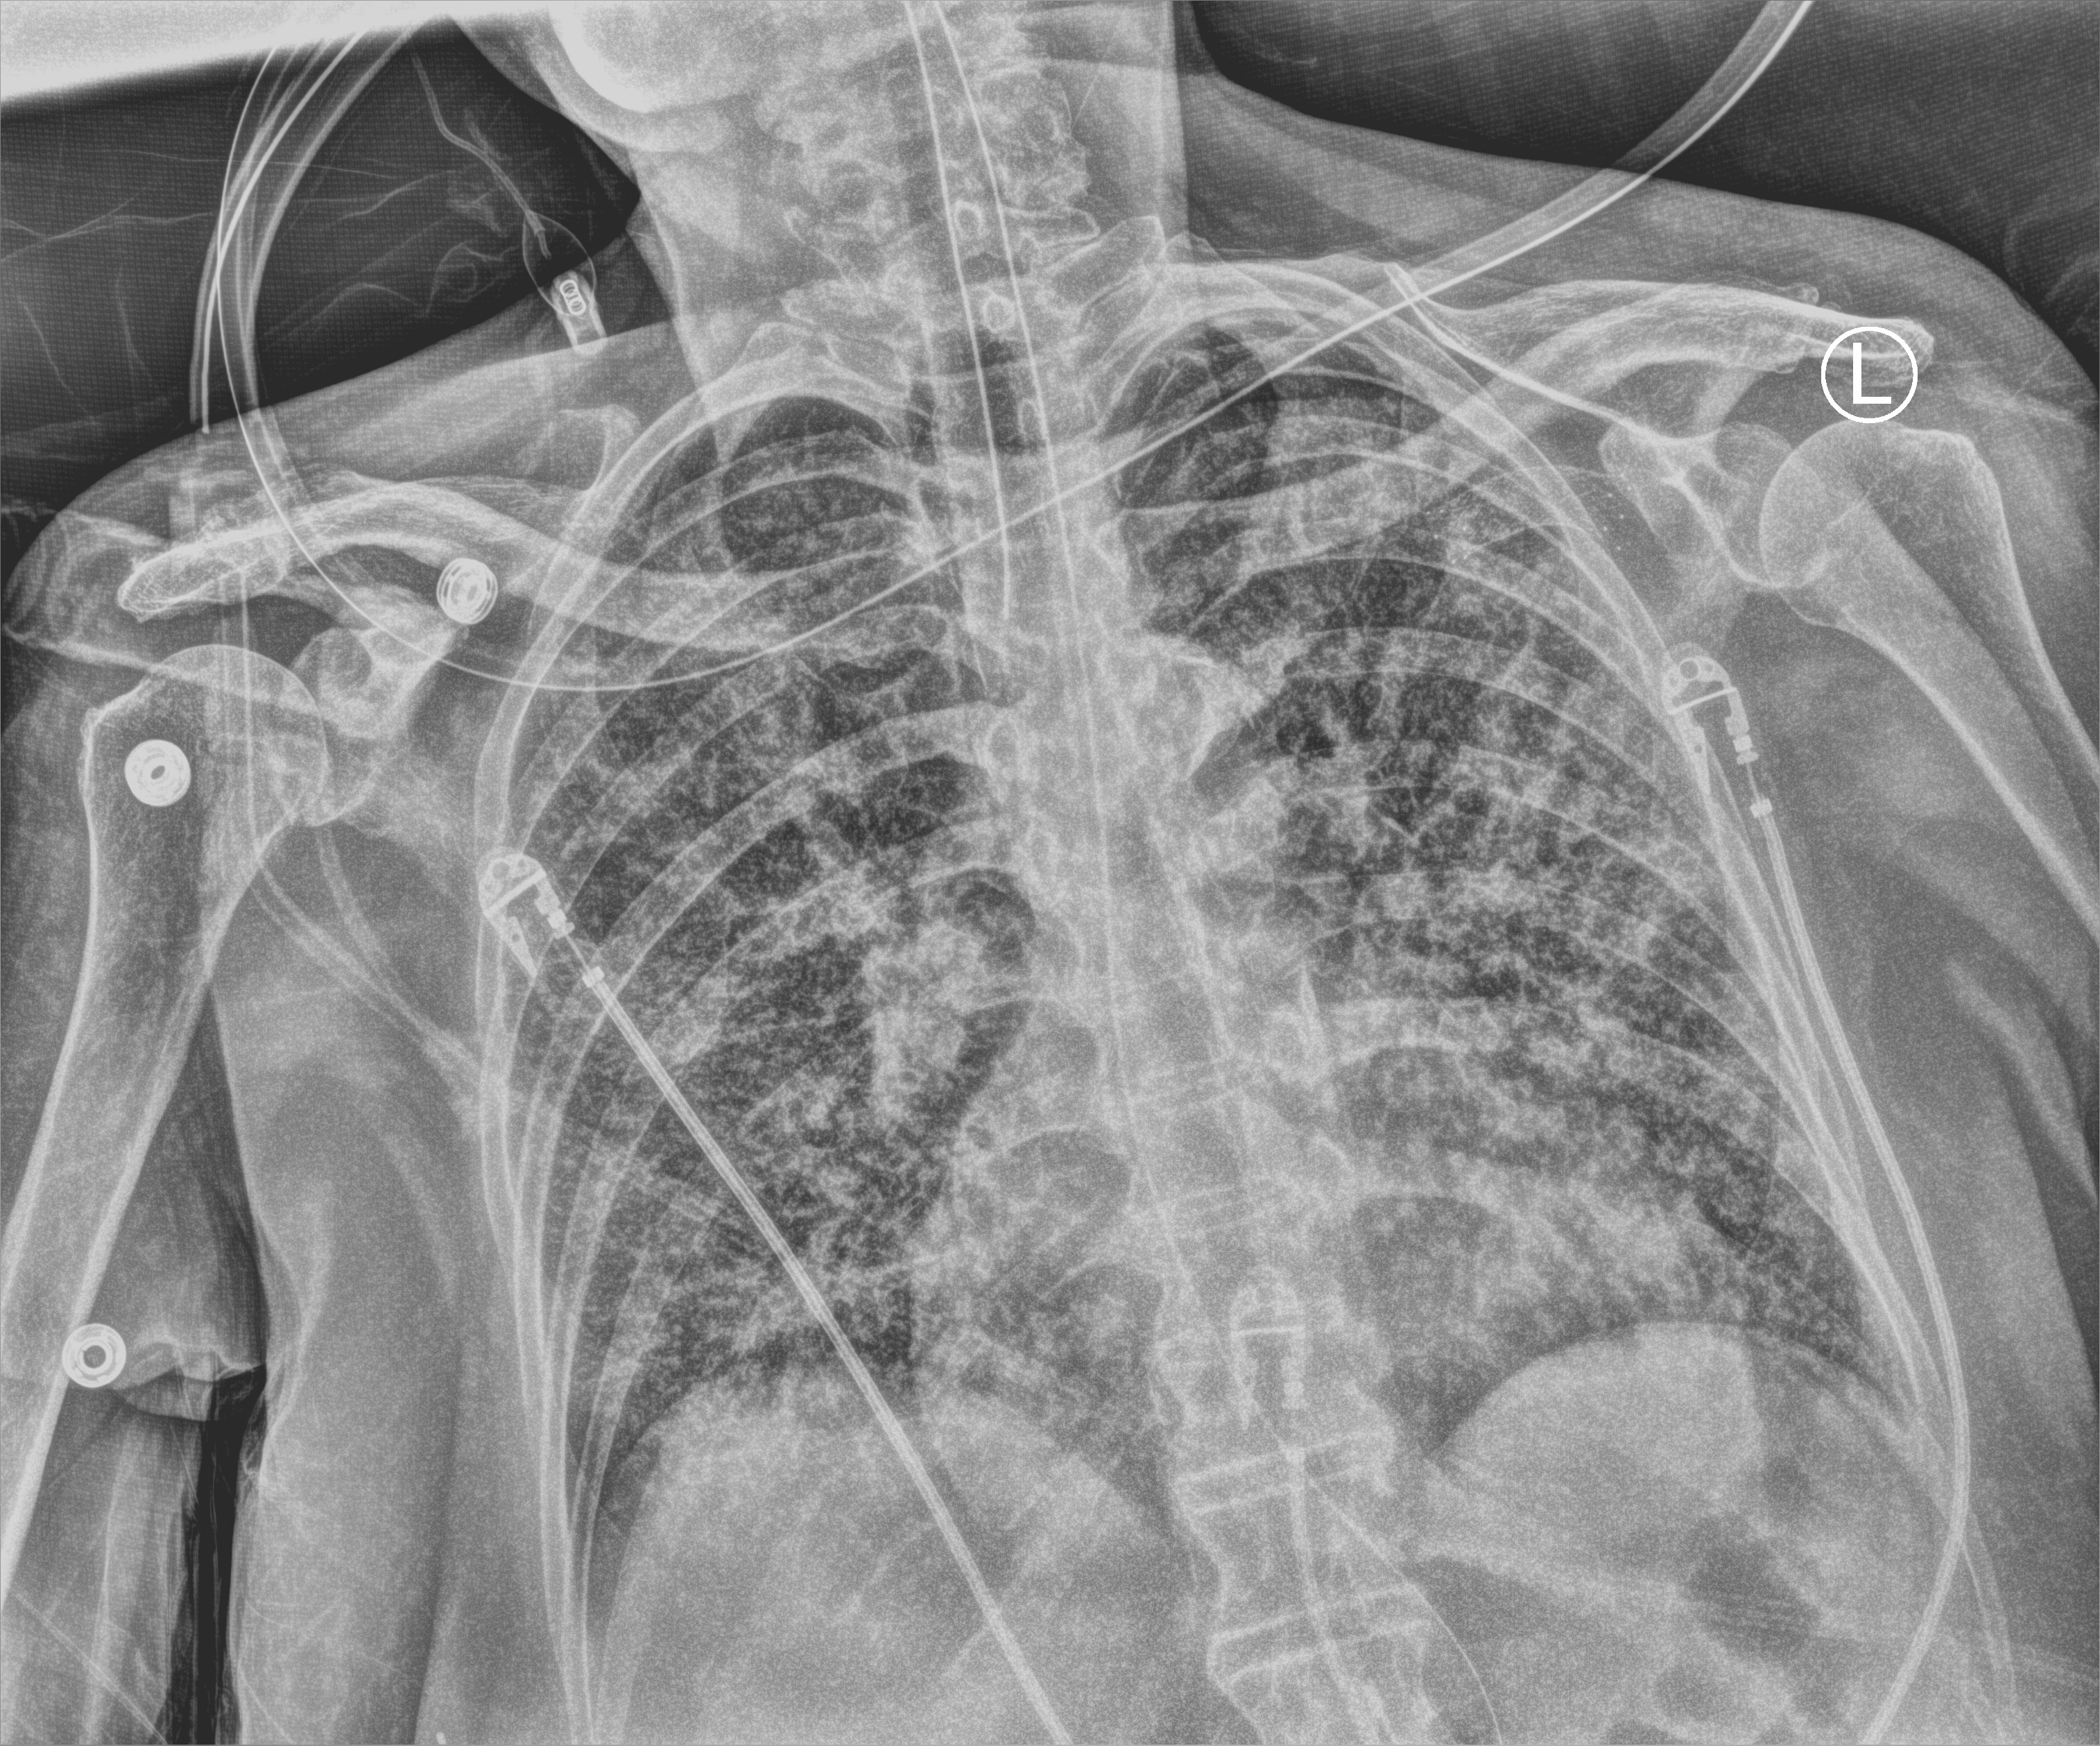
Portable chest radiograph; anteroposterior (AP) projection. Patient hospitalised with COVID-19; female, aged 60–74 years.
Hospital-stay facts (about this admission, not read from this image; timing relative to this image not recorded): mechanically ventilated during this hospital stay: yes; length of hospital stay: 23 days; admitted to intensive care during this hospital stay: yes.